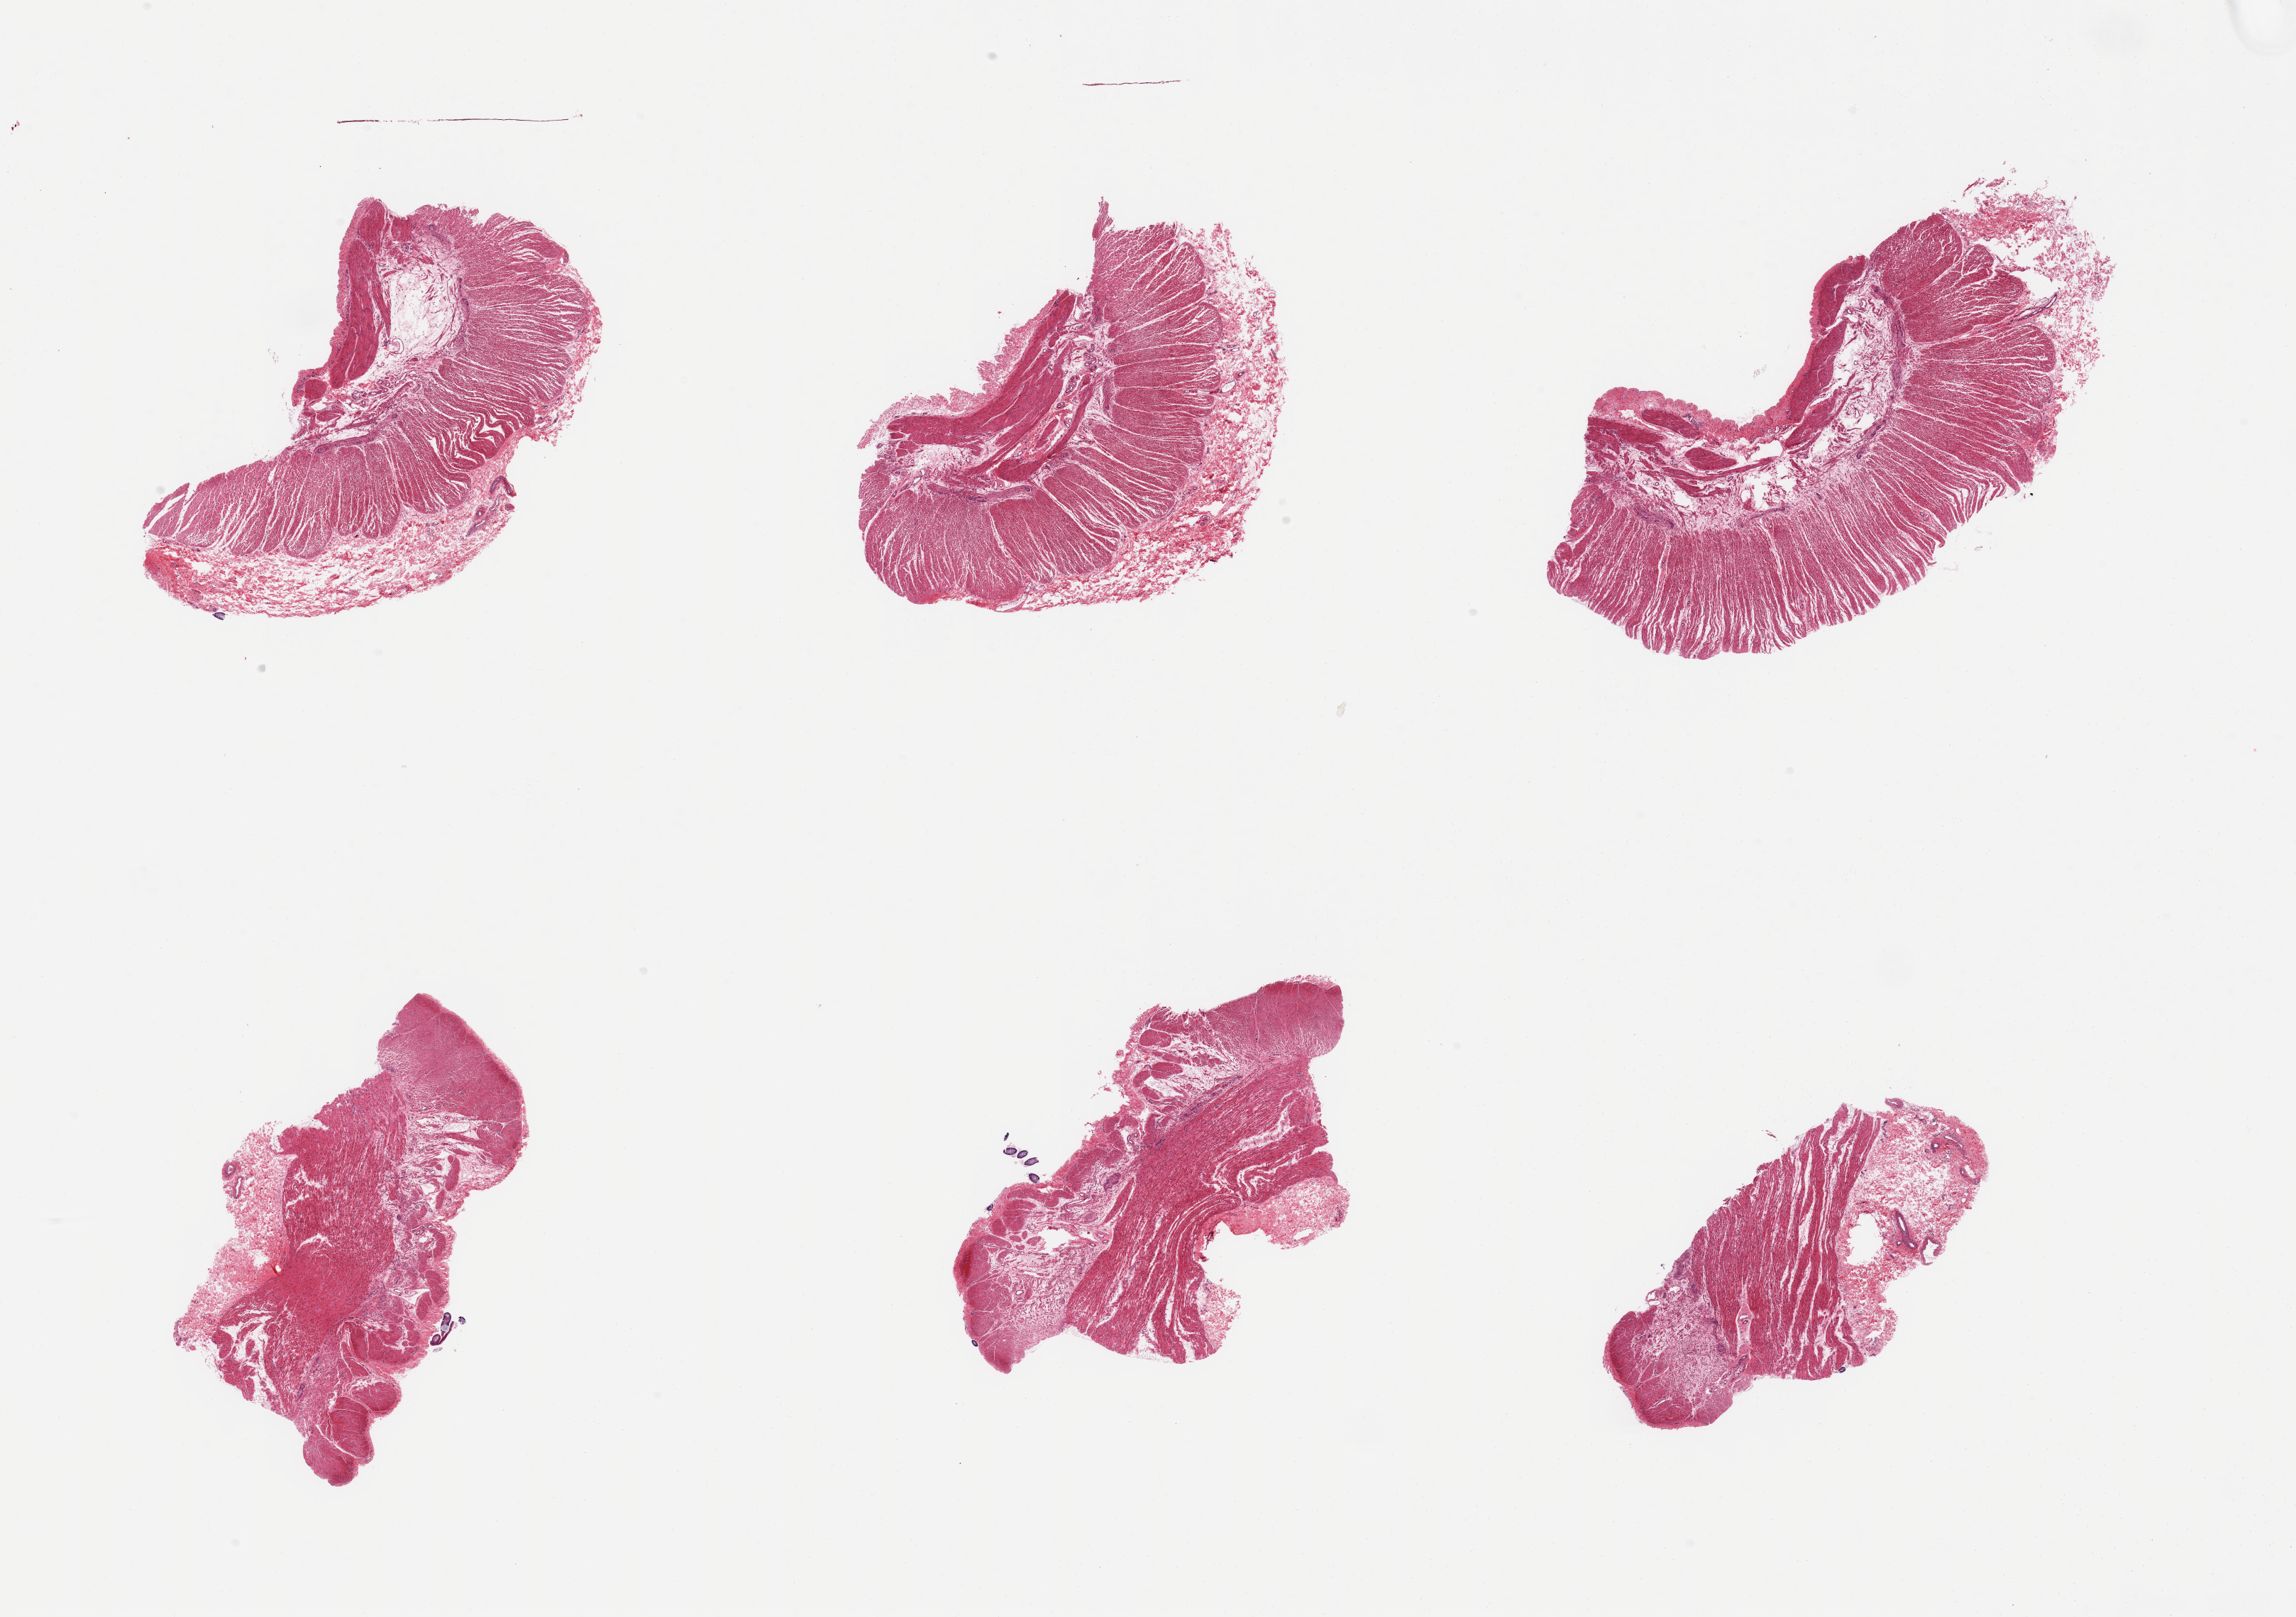
Digitized hematoxylin and eosin (H&E)-stained section, shown as a low-resolution overview of the whole scanned area (about 25.6 x 18.0 mm, acquisition: 20x scan). PAXgene-fixed paraffin-embedded (PFPE) section. Section of sigmoid colon (target tissue). Tissue donor sample. Donor: male.
Reviewer comment on this tissue sample: 6 pieces, confirmed target muscularis.